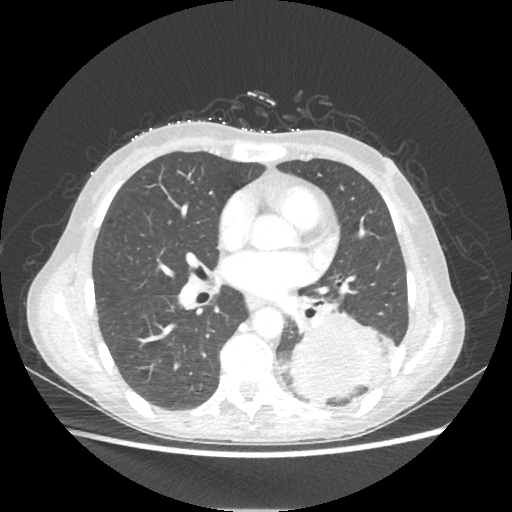
Chest CT, one axial slice; position 106 of 221 along the scan axis; reconstruction kernel STANDARD; 80 kVp; lung window (W 1500 / L -600 HU); 1.25 mm slice thickness; 512 × 512 image matrix, field of view 360 × 360 mm. Patient: female, 53 years. From the clinical record (not read from this slice): clinical TNM (as recorded): T3 N0 M0.
Annotated regions visible in this slice (bounding box drawn by a radiologist):
- lung tumour (recorded histology: adenocarcinoma): bounding box (x1, y1, x2, y2) in pixels: (287, 311, 386, 401)